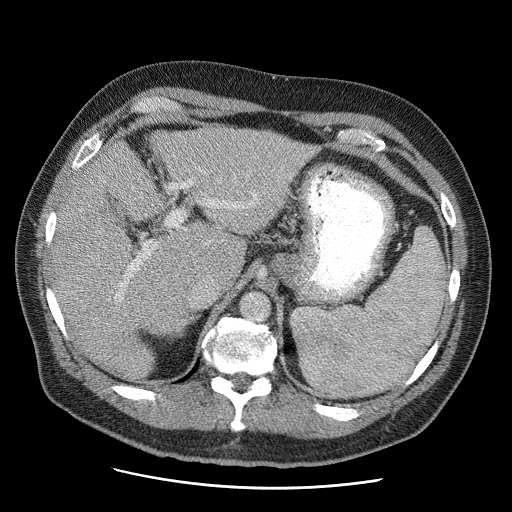
Contrast-enhanced abdominal CT (liver protocol), one axial slice; 120 kVp; soft-tissue window (W 400 / L 40 HU); 2.5 mm slice thickness; 512 × 512 image matrix, field of view 380 × 380 mm. Case-level facts recorded for this patient, not image findings: diagnosis: hepatocellular carcinoma (patient treated with transarterial chemoembolisation; whether this scan precedes or follows treatment is not stated here); TNM stage (as recorded): Stage-IIIA; Child-Pugh class: A; tumour differentiation: moderately differentiated; tumour size: 5.5 cm.
Structures marked on this image (semi-automatically segmented with operator editing):
- liver parenchyma outside the tumour (the mass and vessels are separate outlines, so this box may not span the whole liver): bounding box [x1, y1, x2, y2] px = [51, 124, 314, 378]
- liver vessels: [114, 180, 256, 300]